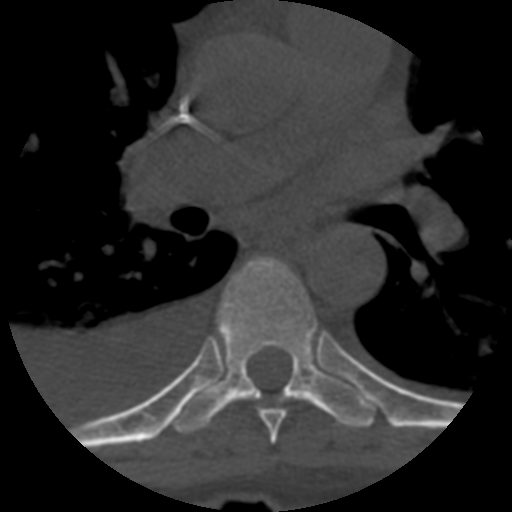
CT including the spine, one axial slice; slice 423 of 708 in the series (ordered by position); one of 3 acquisitions stored at this slice position; bone window (W 1800 / L 400 HU); 512 × 512 image matrix. Patient age 55 years. Case-level facts recorded for this patient, not image findings: primary cancer: colon; vertebrae with lytic lesions (as recorded): T12, L1, L5.
Annotated regions visible in this slice (semi-automatic segmentation, software-assisted and operator-edited):
- T6 vertebra: bounding box (x1, y1, x2, y2) in pixels: (258, 408, 287, 444)
- T7 vertebra: (173, 259, 376, 435)